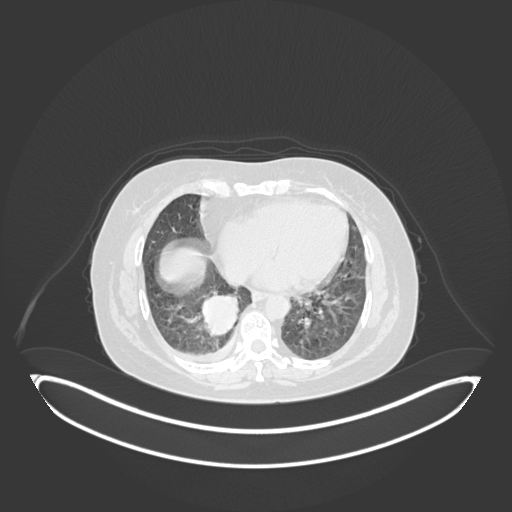
Chest CT, one axial slice; position 52 of 231 along the scan axis; lung window (W 1500 / L -600 HU); 1 mm slice thickness; 512 × 512 image matrix, field of view 500 × 500 mm. Female patient, age 56 years. Case-level facts recorded for this patient, not image findings: clinical TNM (as recorded): T2b N1 M0; histopathological grade: G3.
Structures marked on this image (bounding box drawn by a radiologist):
- lung tumour (recorded histology: small cell carcinoma): bounding box [x1, y1, x2, y2] px = [201, 289, 244, 340]